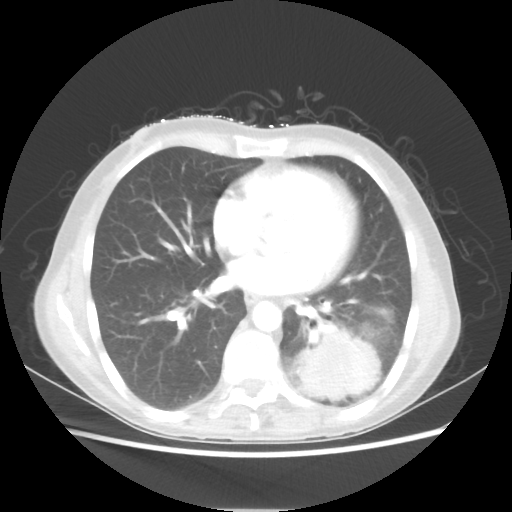
Chest CT, one axial slice. Position 24 of 56 along the scan axis. 80 kVp. Lung window (W 1500 / L -600 HU). 512 × 512 image matrix, field of view 360 × 360 mm. Patient: female, 53 years. From the clinical record (not read from this slice): clinical TNM (as recorded): T3 N0 M0.
Annotated regions visible in this slice (rectangle marked by the reading radiologist):
- lung tumour (recorded histology: adenocarcinoma): bounding box (x1, y1, x2, y2) in pixels: (296, 332, 380, 400)